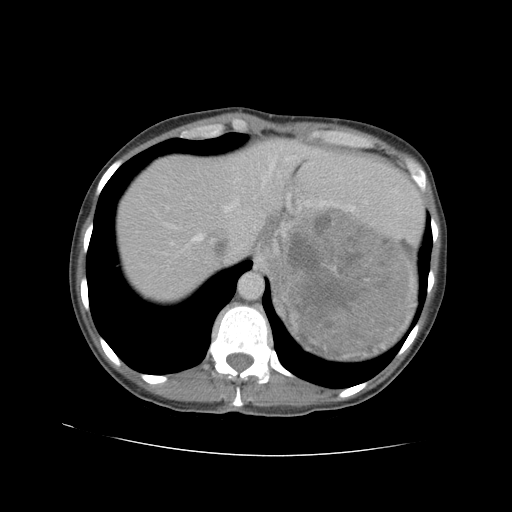
Contrast-enhanced abdominal CT, one axial slice; position 78 of 90 along the scan axis; 120 kVp; intravenous contrast given; soft-tissue window (W 400 / L 40 HU); 5 mm slice thickness; 512 × 512 image matrix. Female patient. From the clinical record (not read from this slice): diagnosis: adrenocortical carcinoma; tumour side: left adrenal; tumour size at pathology: 18 cm; Ki-67 index: 11 %; stage (as recorded): 3.
Annotated regions visible in this slice (semi-automatically segmented with operator editing):
- mass: bounding box (x1, y1, x2, y2) in pixels: (273, 215, 410, 354)